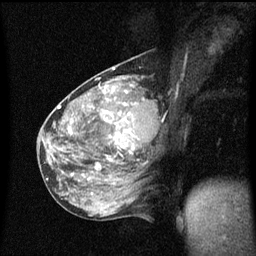
Breast MRI (dynamic contrast-enhanced), one sagittal slice; position 25 of 60 along the scan axis; dynamic contrast-enhanced series, image 2 of 3 at this slice position (ordered by acquisition); 1.5 T; TE 4.2 ms, TR 8.4 ms; 256 × 256 image matrix, field of view 200 × 200 mm. Female patient, age 49 years.
Structures marked on this image (semi-automatic segmentation, software-assisted and operator-edited):
- analysis volume of interest (the breast-tissue region the enhancement analysis was run in; not a lesion): bounding box (x1, y1, x2, y2) in pixels: (103, 90, 157, 151)
- tumour enhancement mask (voxels above the 70 % enhancement threshold inside the analysis volume of interest): (106, 92, 135, 149)